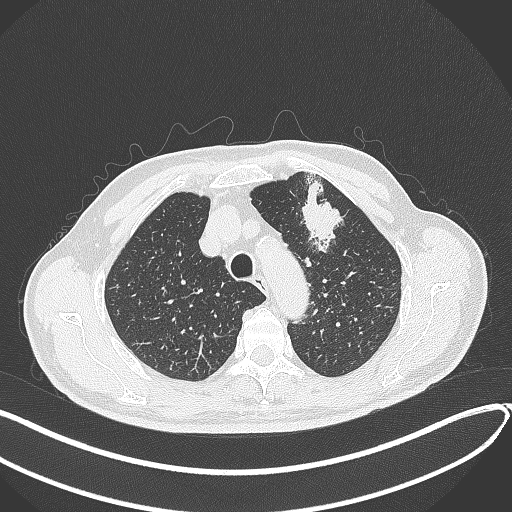
Chest CT, one axial slice; reconstruction kernel B70f; 120 kVp; lung window (W 1500 / L -600 HU); 1 mm slice thickness; 512 × 512 image matrix. Male patient, age 74 years. From the clinical record (not read from this slice): clinical TNM (as recorded): T2b N0 M1c.
Annotated regions visible in this slice (bounding box drawn by a radiologist):
- lung tumour (recorded histology: adenocarcinoma): bounding box <297,172,352,257> (left, top, right, bottom; pixels)